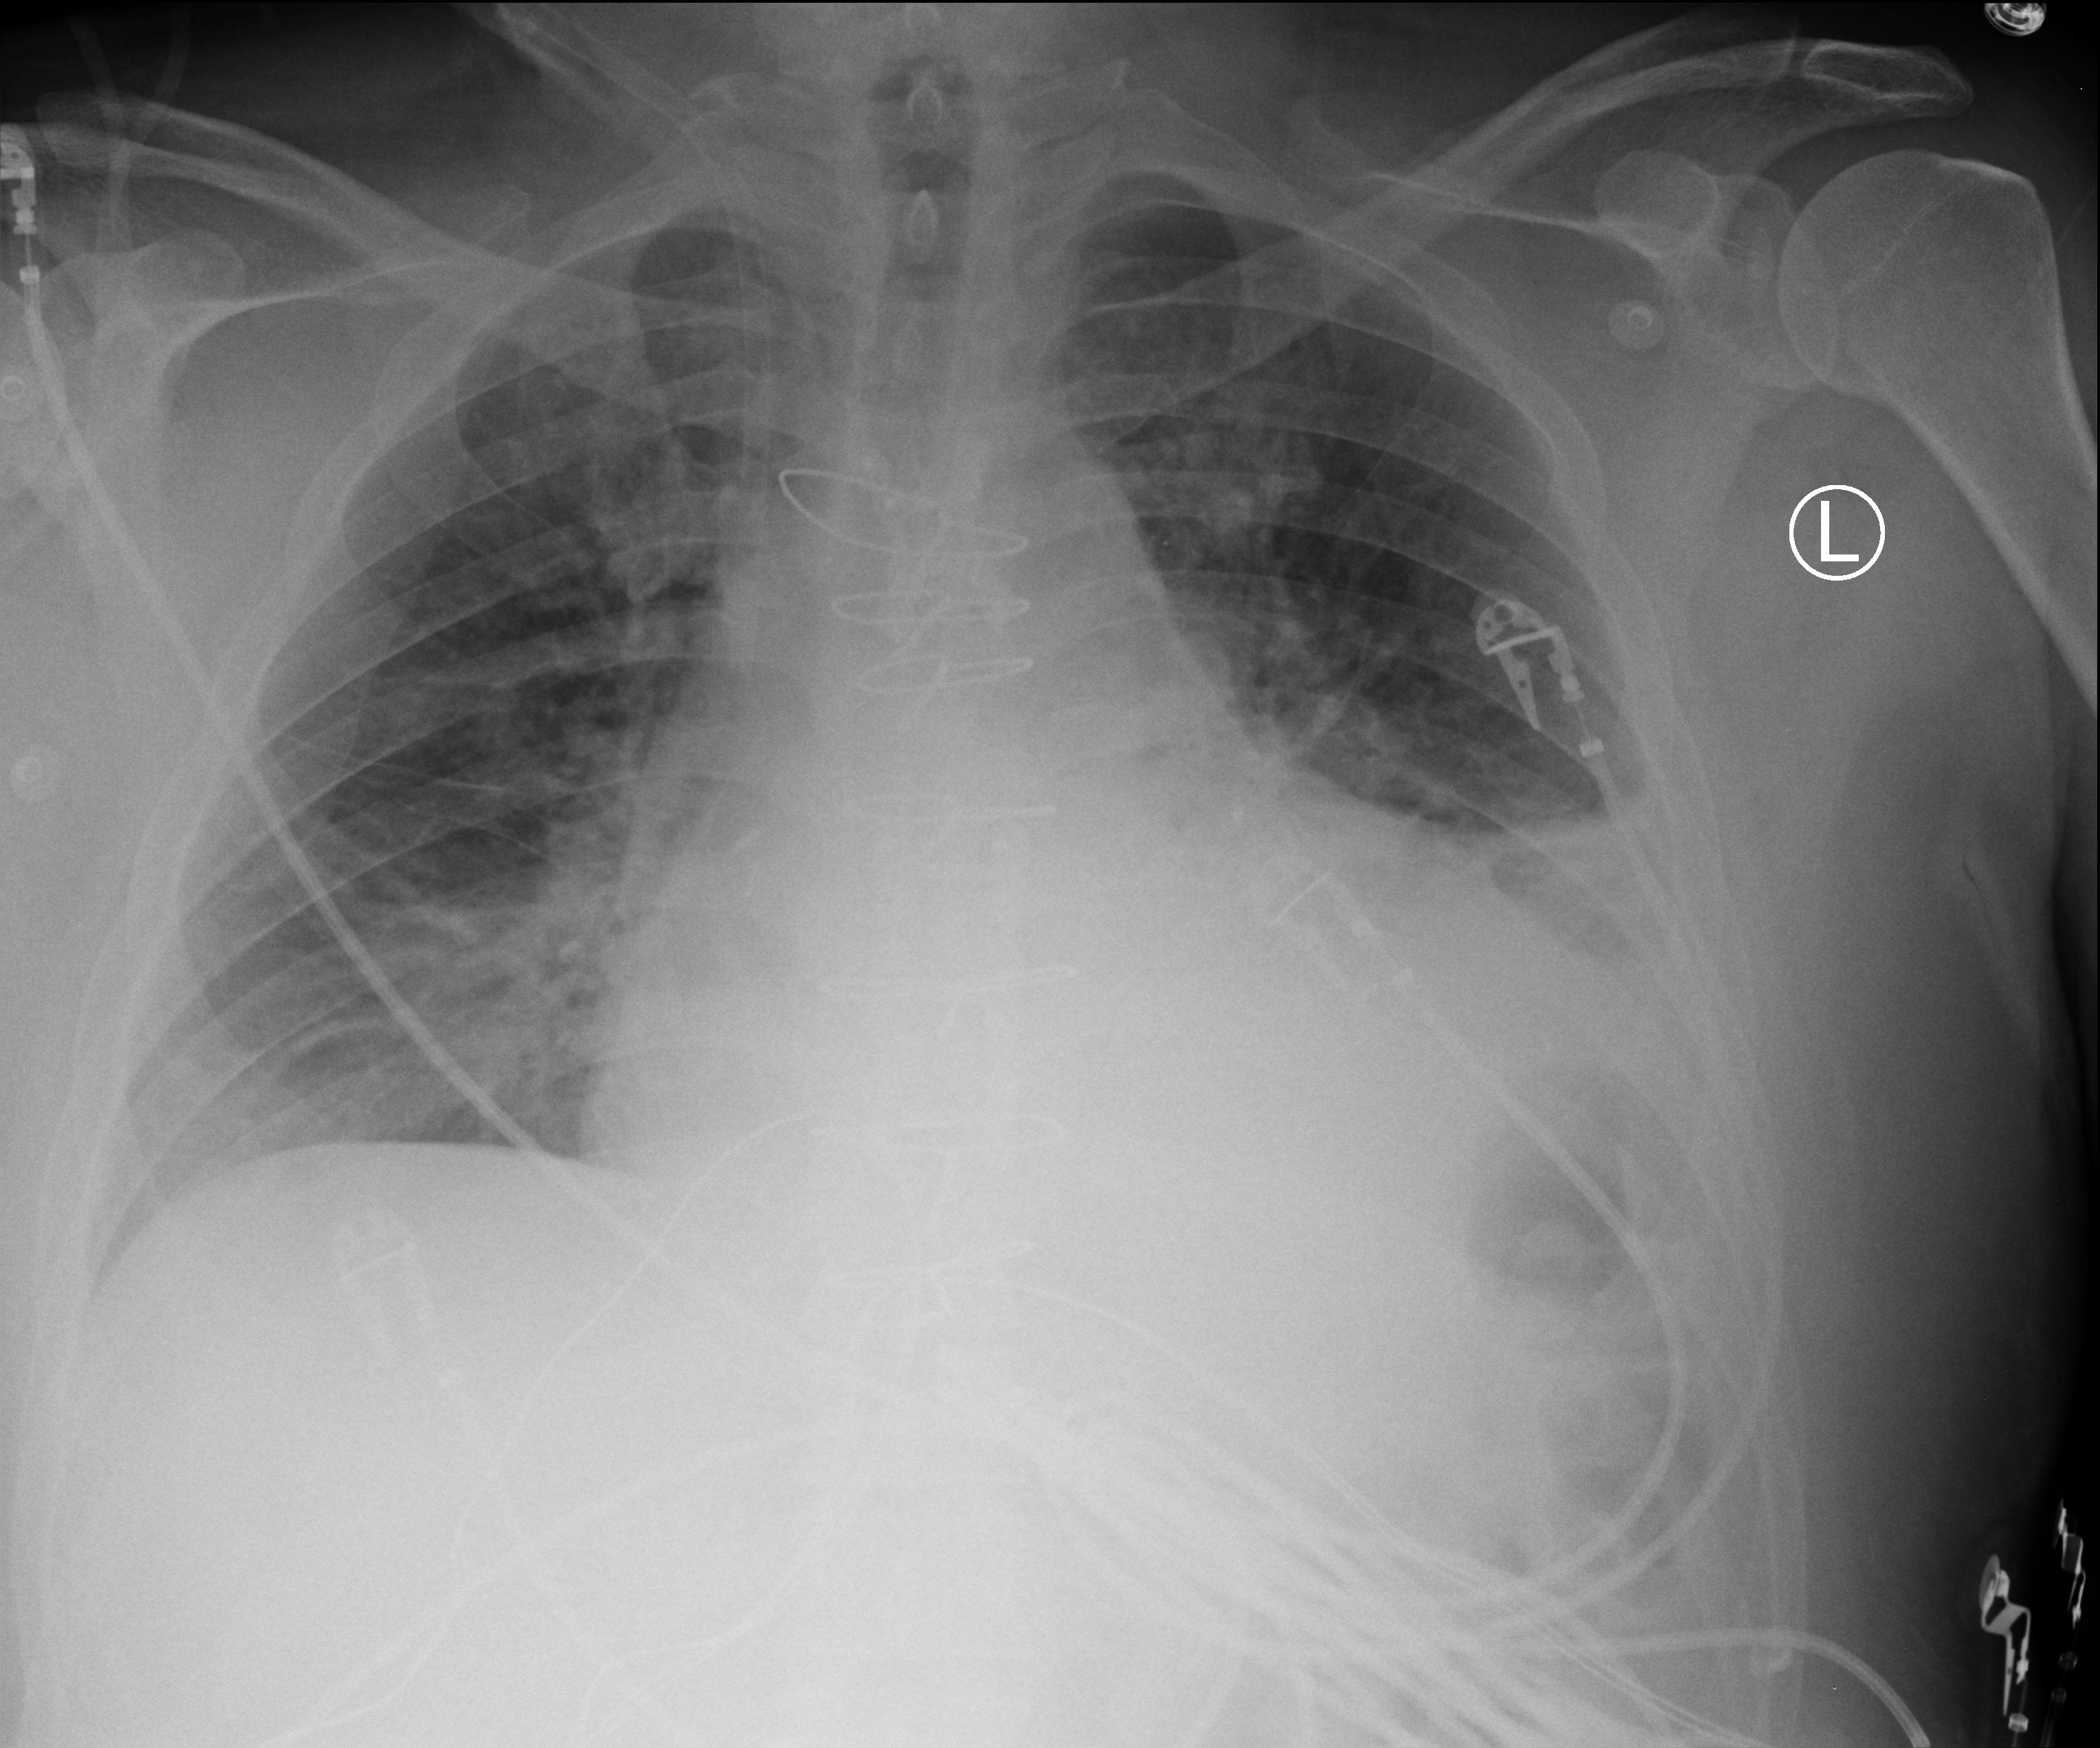
Chest X-ray (portable). Male patient hospitalised with COVID-19, age 18–59 years.
Admission-level facts for this patient (not findings on this image; timing relative to this image not recorded): admitted to intensive care during this hospital stay: no.